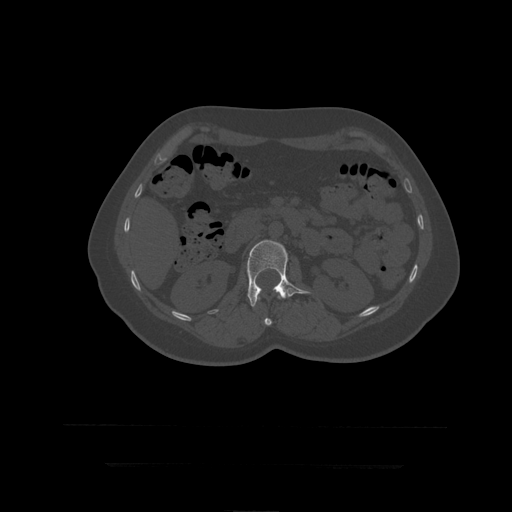
CT including the spine, one axial slice; position 154 of 399 along the scan axis; 120 kVp; bone window (W 1800 / L 400 HU); 1.25 mm slice thickness; 512 × 512 image matrix, field of view 450 × 450 mm. Patient age 41 years. From the clinical record (not read from this slice): primary cancer: breast.
Outlined on this slice (semi-automatically segmented with operator editing):
- L1 vertebra: bounding box <264,296,281,326> (left, top, right, bottom; pixels)
- L2 vertebra: <247,240,311,308>